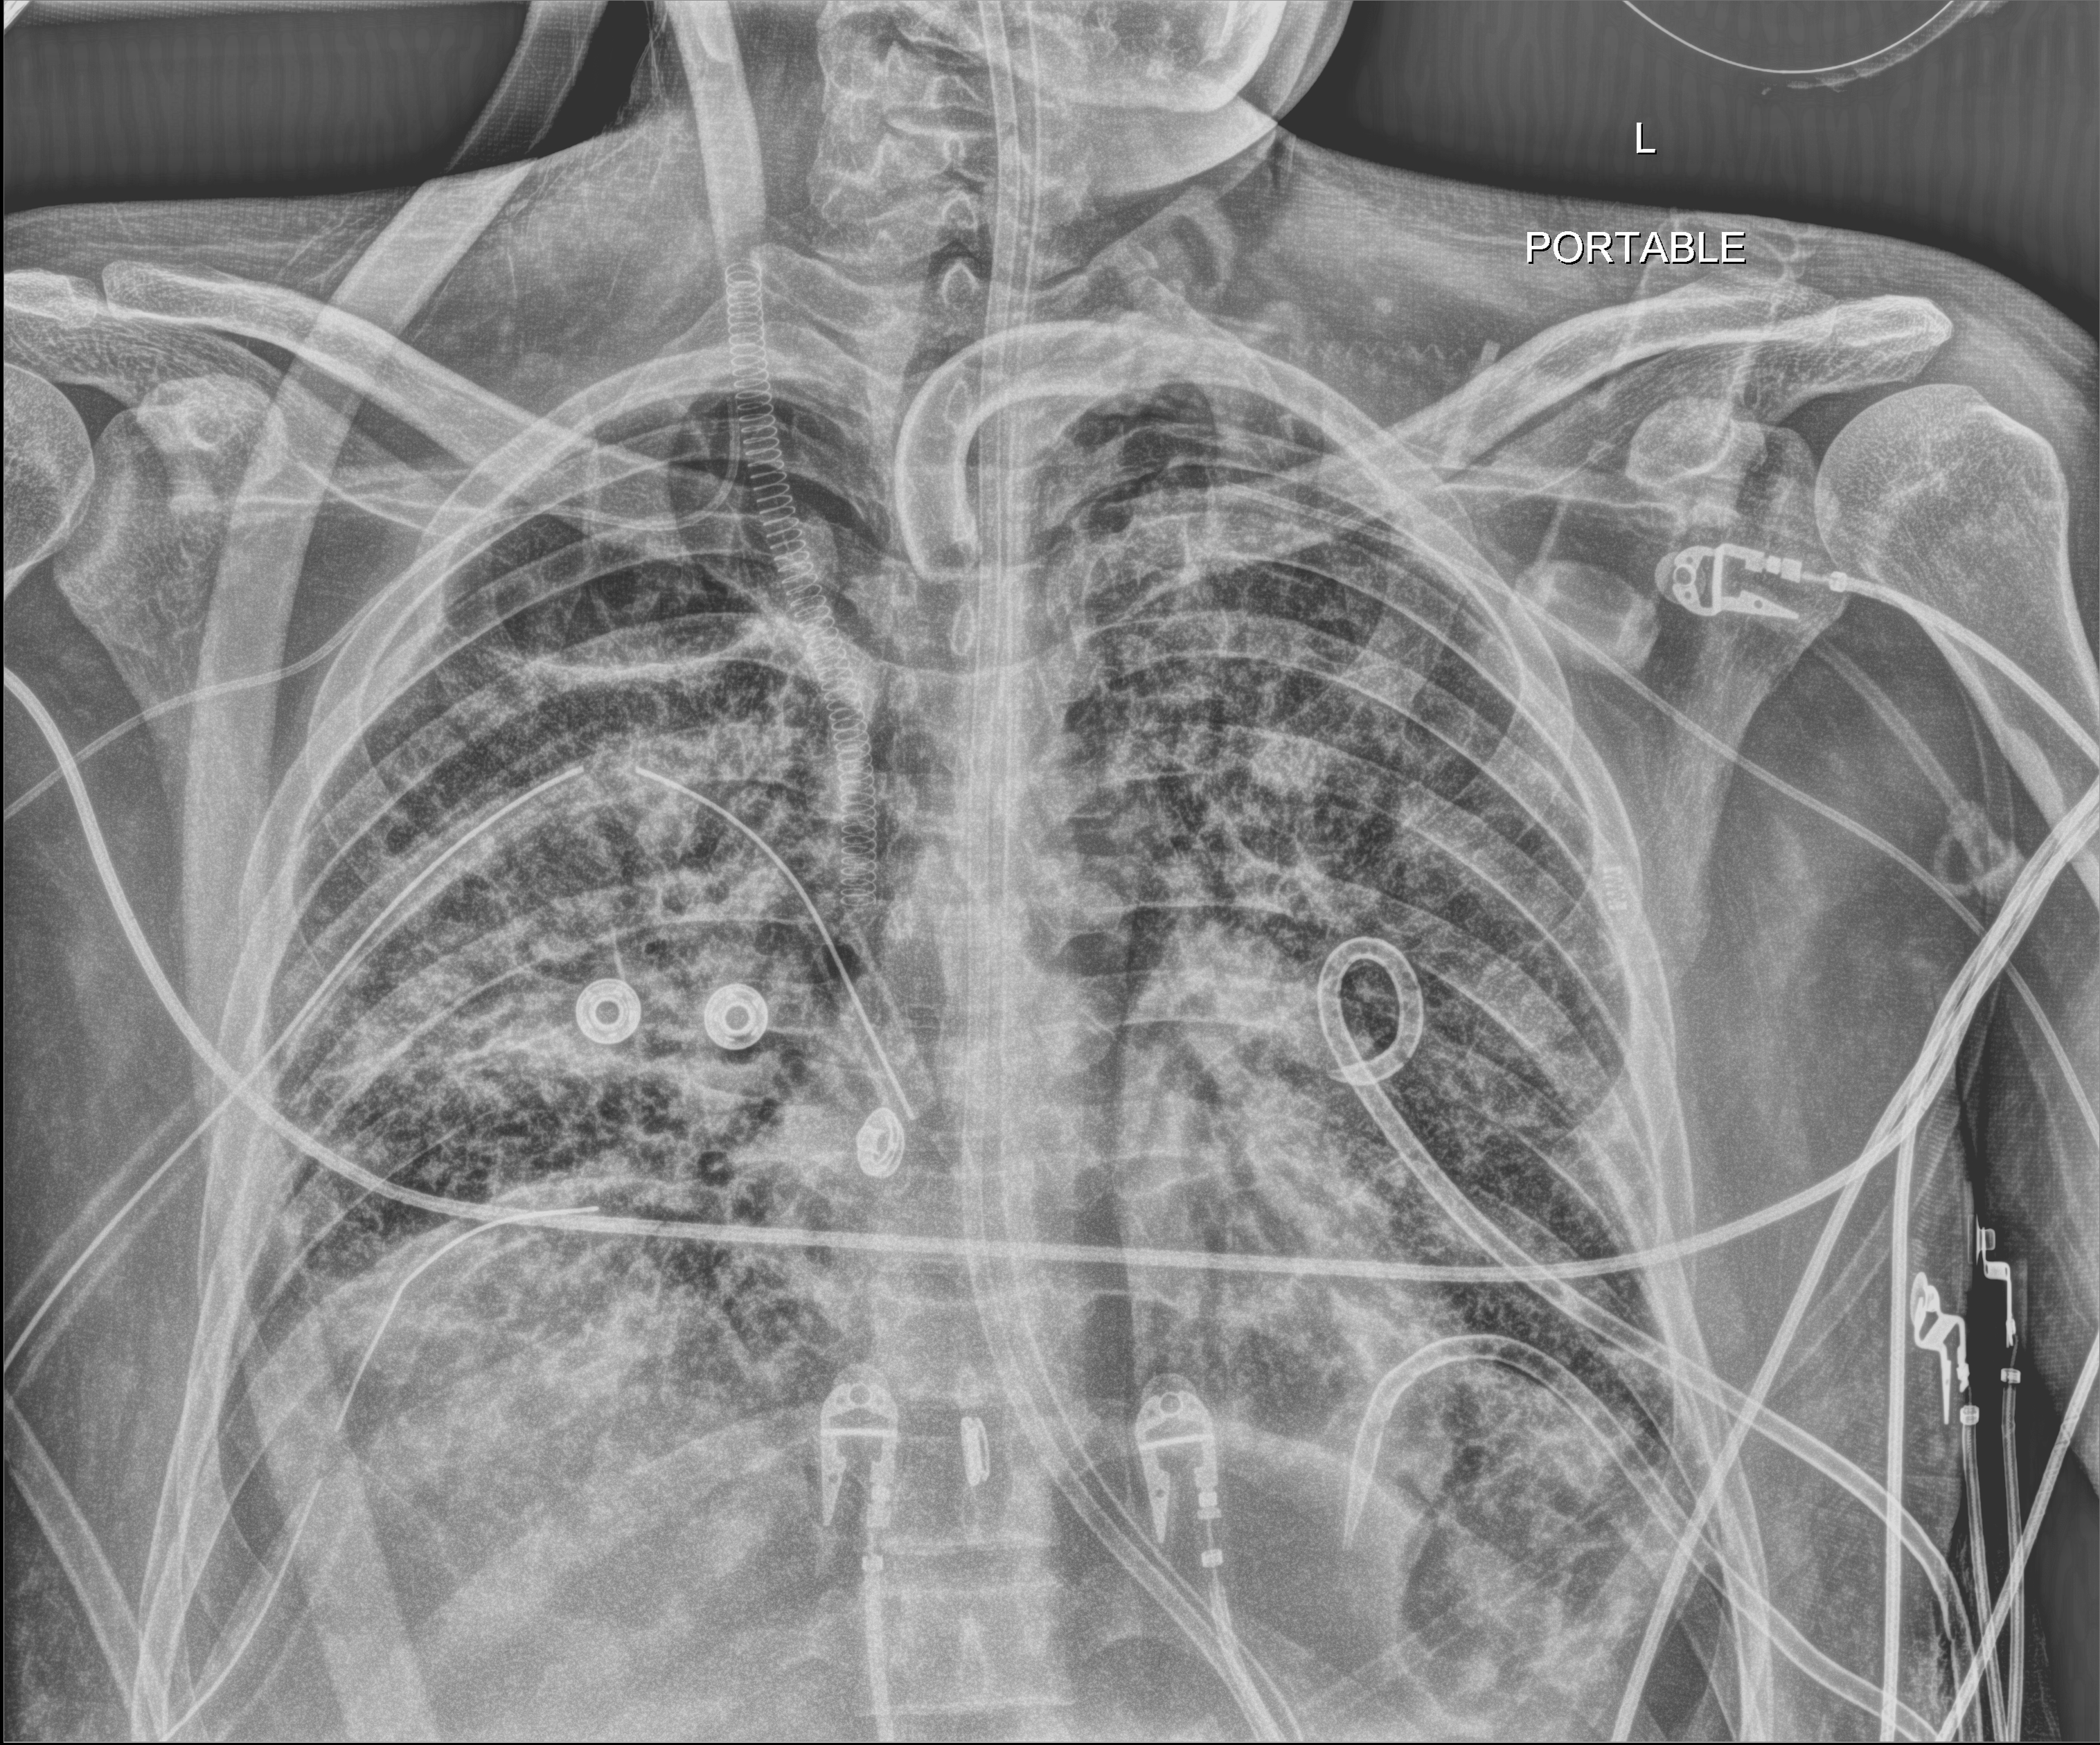
Bedside chest radiograph (digital radiography), anteroposterior (AP) projection. Adult patient hospitalised with COVID-19, age 18–59 years.
From the hospital-stay record, not from the radiograph (when in the stay this image was taken is not recorded): smoking status (admission record): never; mechanically ventilated during this hospital stay: yes.